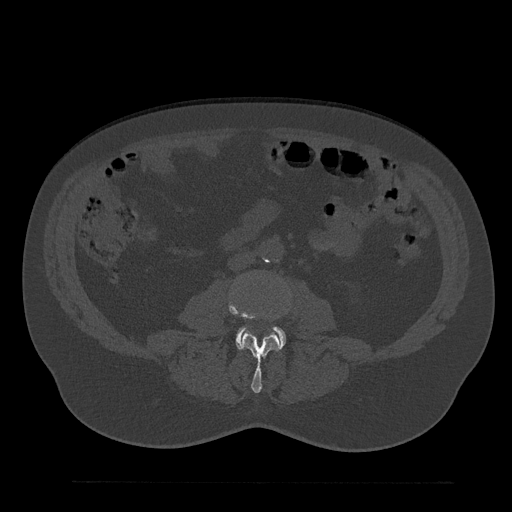
CT including the spine, one axial slice. Slice 6 of 797 in the series (ordered by position). 120 kVp. Bone window (W 1800 / L 400 HU). 0.5 mm slice thickness. 512 × 512 image matrix, field of view 430 × 430 mm. Patient: male, 61 years. Case-level facts recorded for this patient, not image findings: primary cancer: prostate.
Structures marked on this image (semi-automatic segmentation, software-assisted and operator-edited):
- L3 vertebra: bounding box (x1, y1, x2, y2) in pixels: (228, 299, 291, 393)
- L4 vertebra: (236, 327, 285, 349)